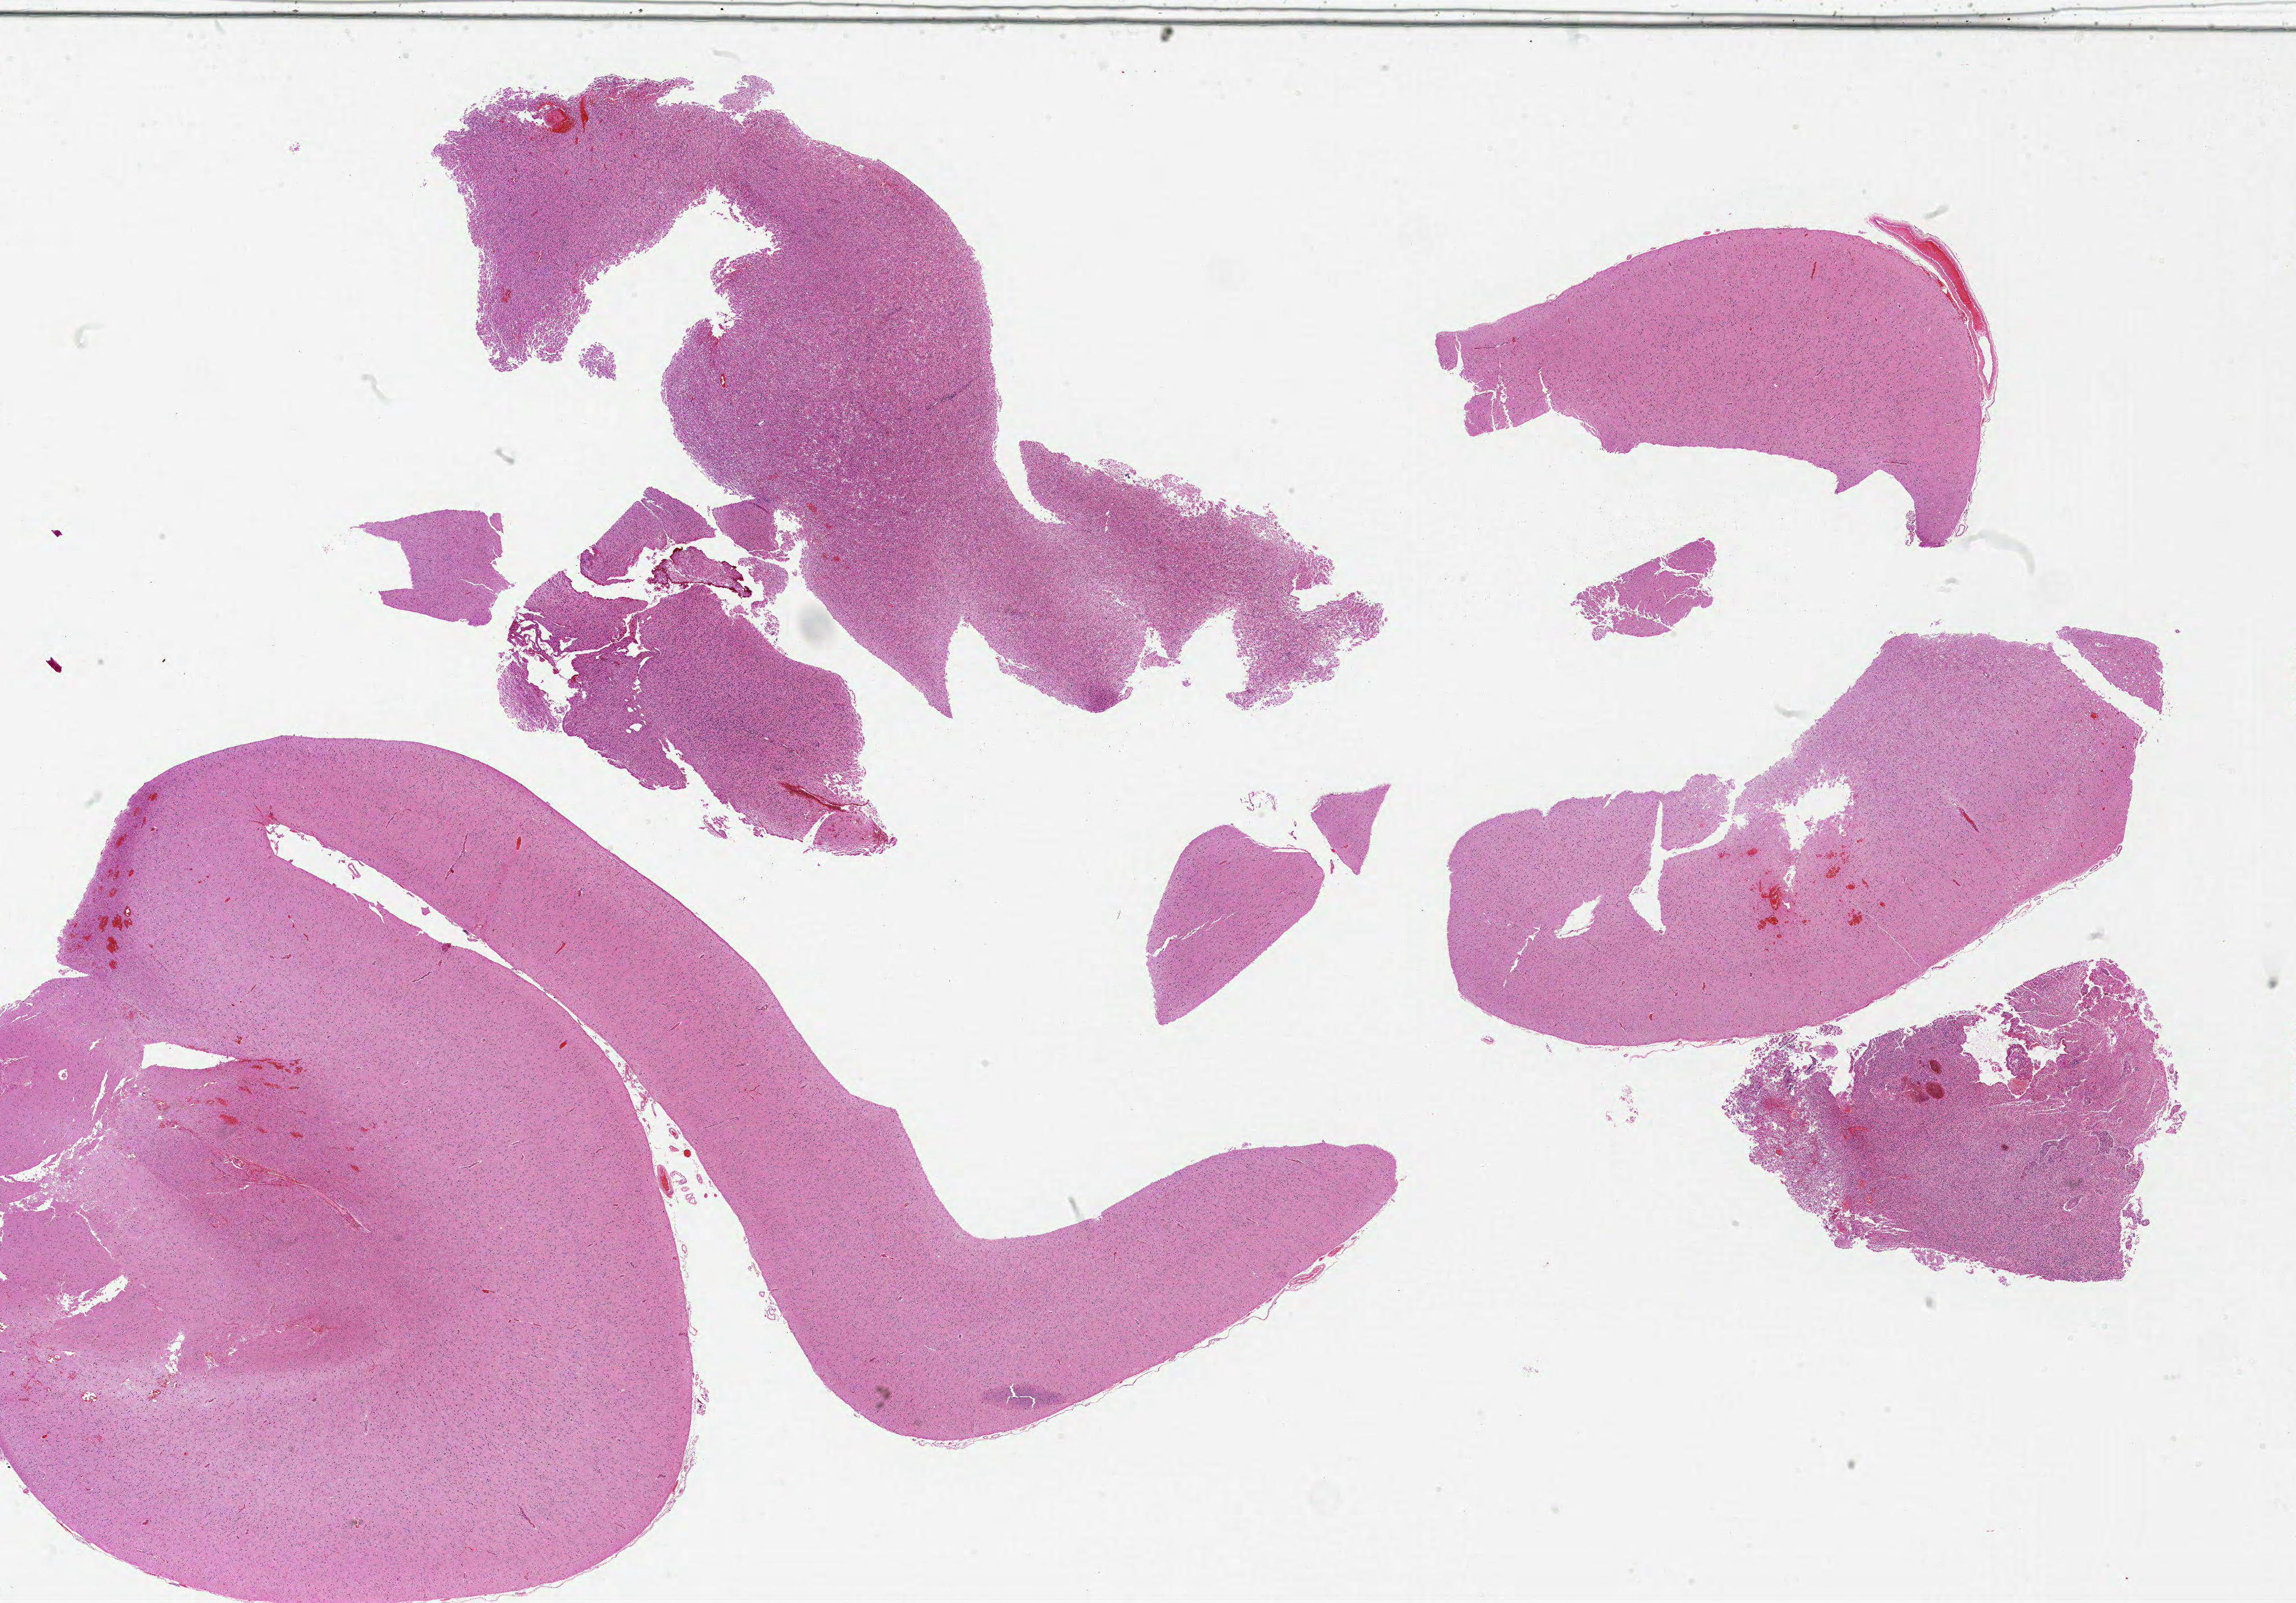
Whole-slide histology image, H&E-stained — whole scanned area (about 32.0 x 22.3 mm) shown as a low-resolution overview; formalin-fixed paraffin-embedded (FFPE) diagnostic section; primary tumour sample from the brain. Patient: female, age at initial diagnosis 75 years.
Diagnosis: Glioblastoma.